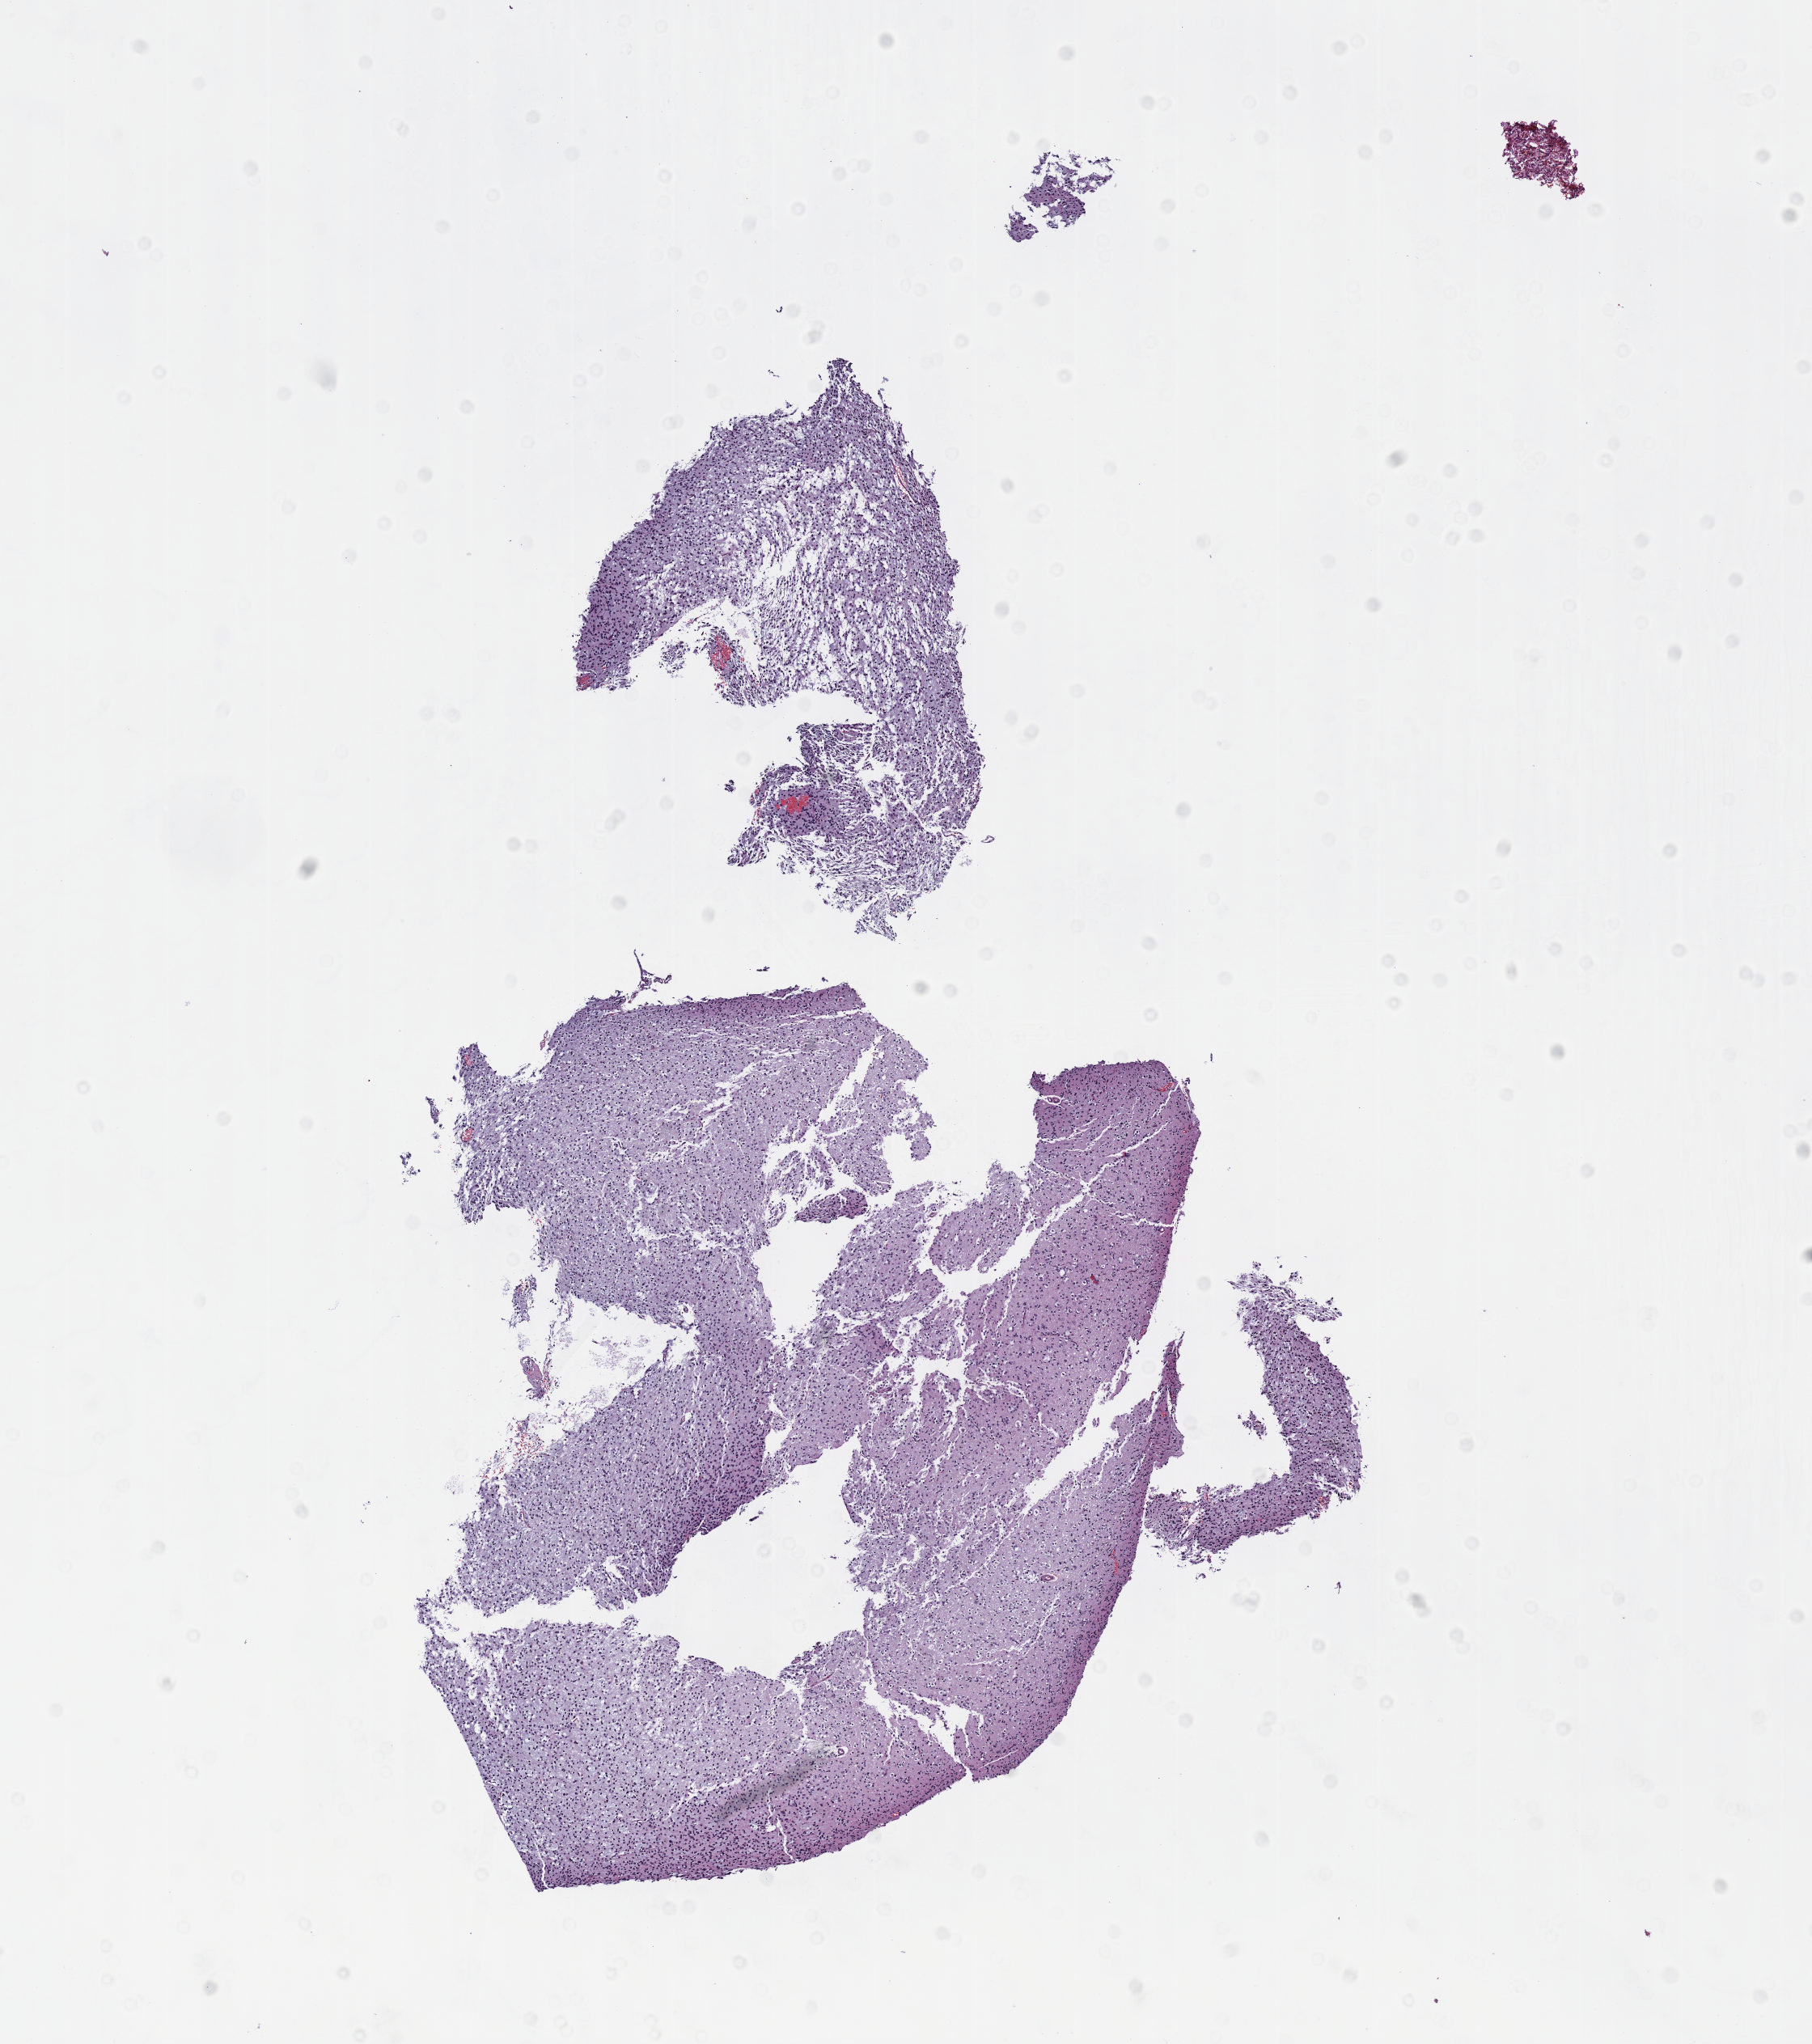
Digitized H&E-stained tissue section (whole slide) — a low-resolution overview of the entire scanned area, about 9.1 x 10.2 mm (from a 40x scan); formalin-fixed paraffin-embedded (FFPE) diagnostic section; brain, primary tumour sample. Female, age 50 years at initial diagnosis. Histologic grade: G2 (moderately differentiated).
Diagnosis: Oligodendroglioma, NOS (cerebrum). Laterality: right.